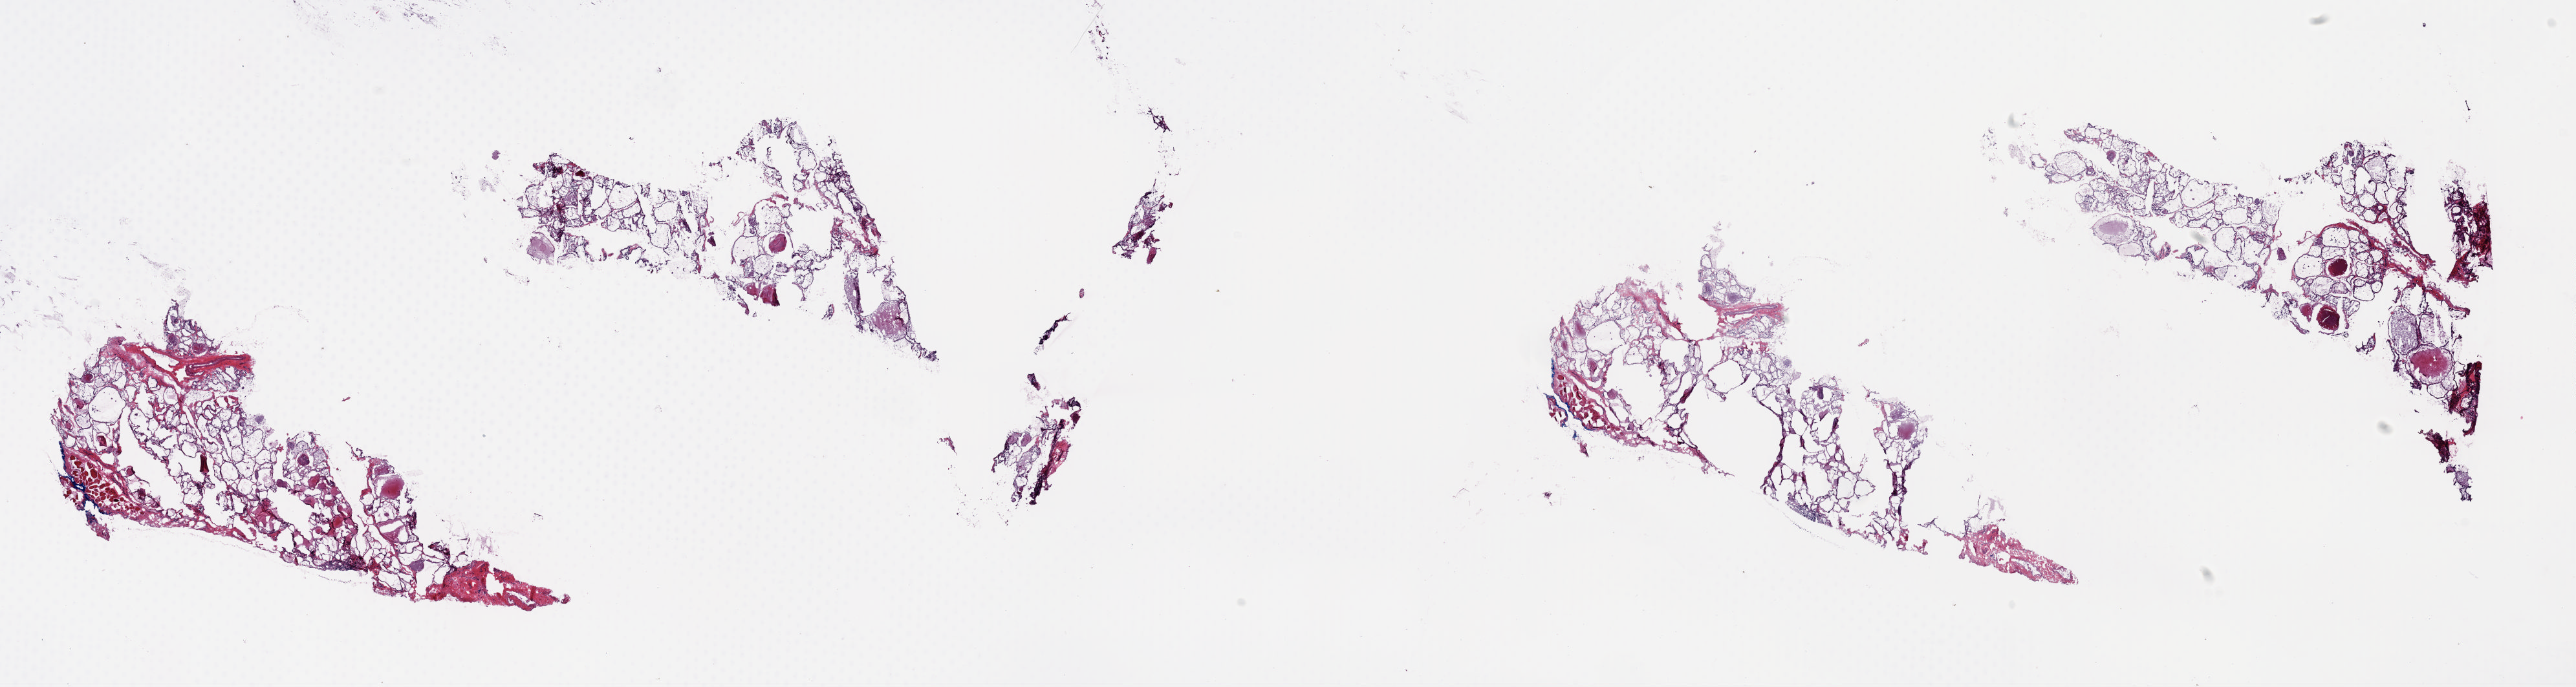
Whole-slide histology image, Hematoxylin and eosin (H&E) stained, a low-resolution overview of the entire scanned area, about 31.4 x 8.4 mm, frozen section from the top of the tissue portion, thyroid, solid tissue normal (non-tumour tissue) sample. Patient: female, age at initial diagnosis 41 years. Pathologist review of this section (percent, as recorded): tumour cells 0%, tumour nuclei 0%, normal cells 100%, stromal cells 0%, necrosis 0%. Infiltration values recorded for this section: lymphocyte infiltration 0%, monocyte infiltration 0%, neutrophil infiltration 0%.
This section: solid tissue normal (non-tumour) sample from the same patient. Patient diagnosis: Papillary adenocarcinoma, NOS (thyroid gland).